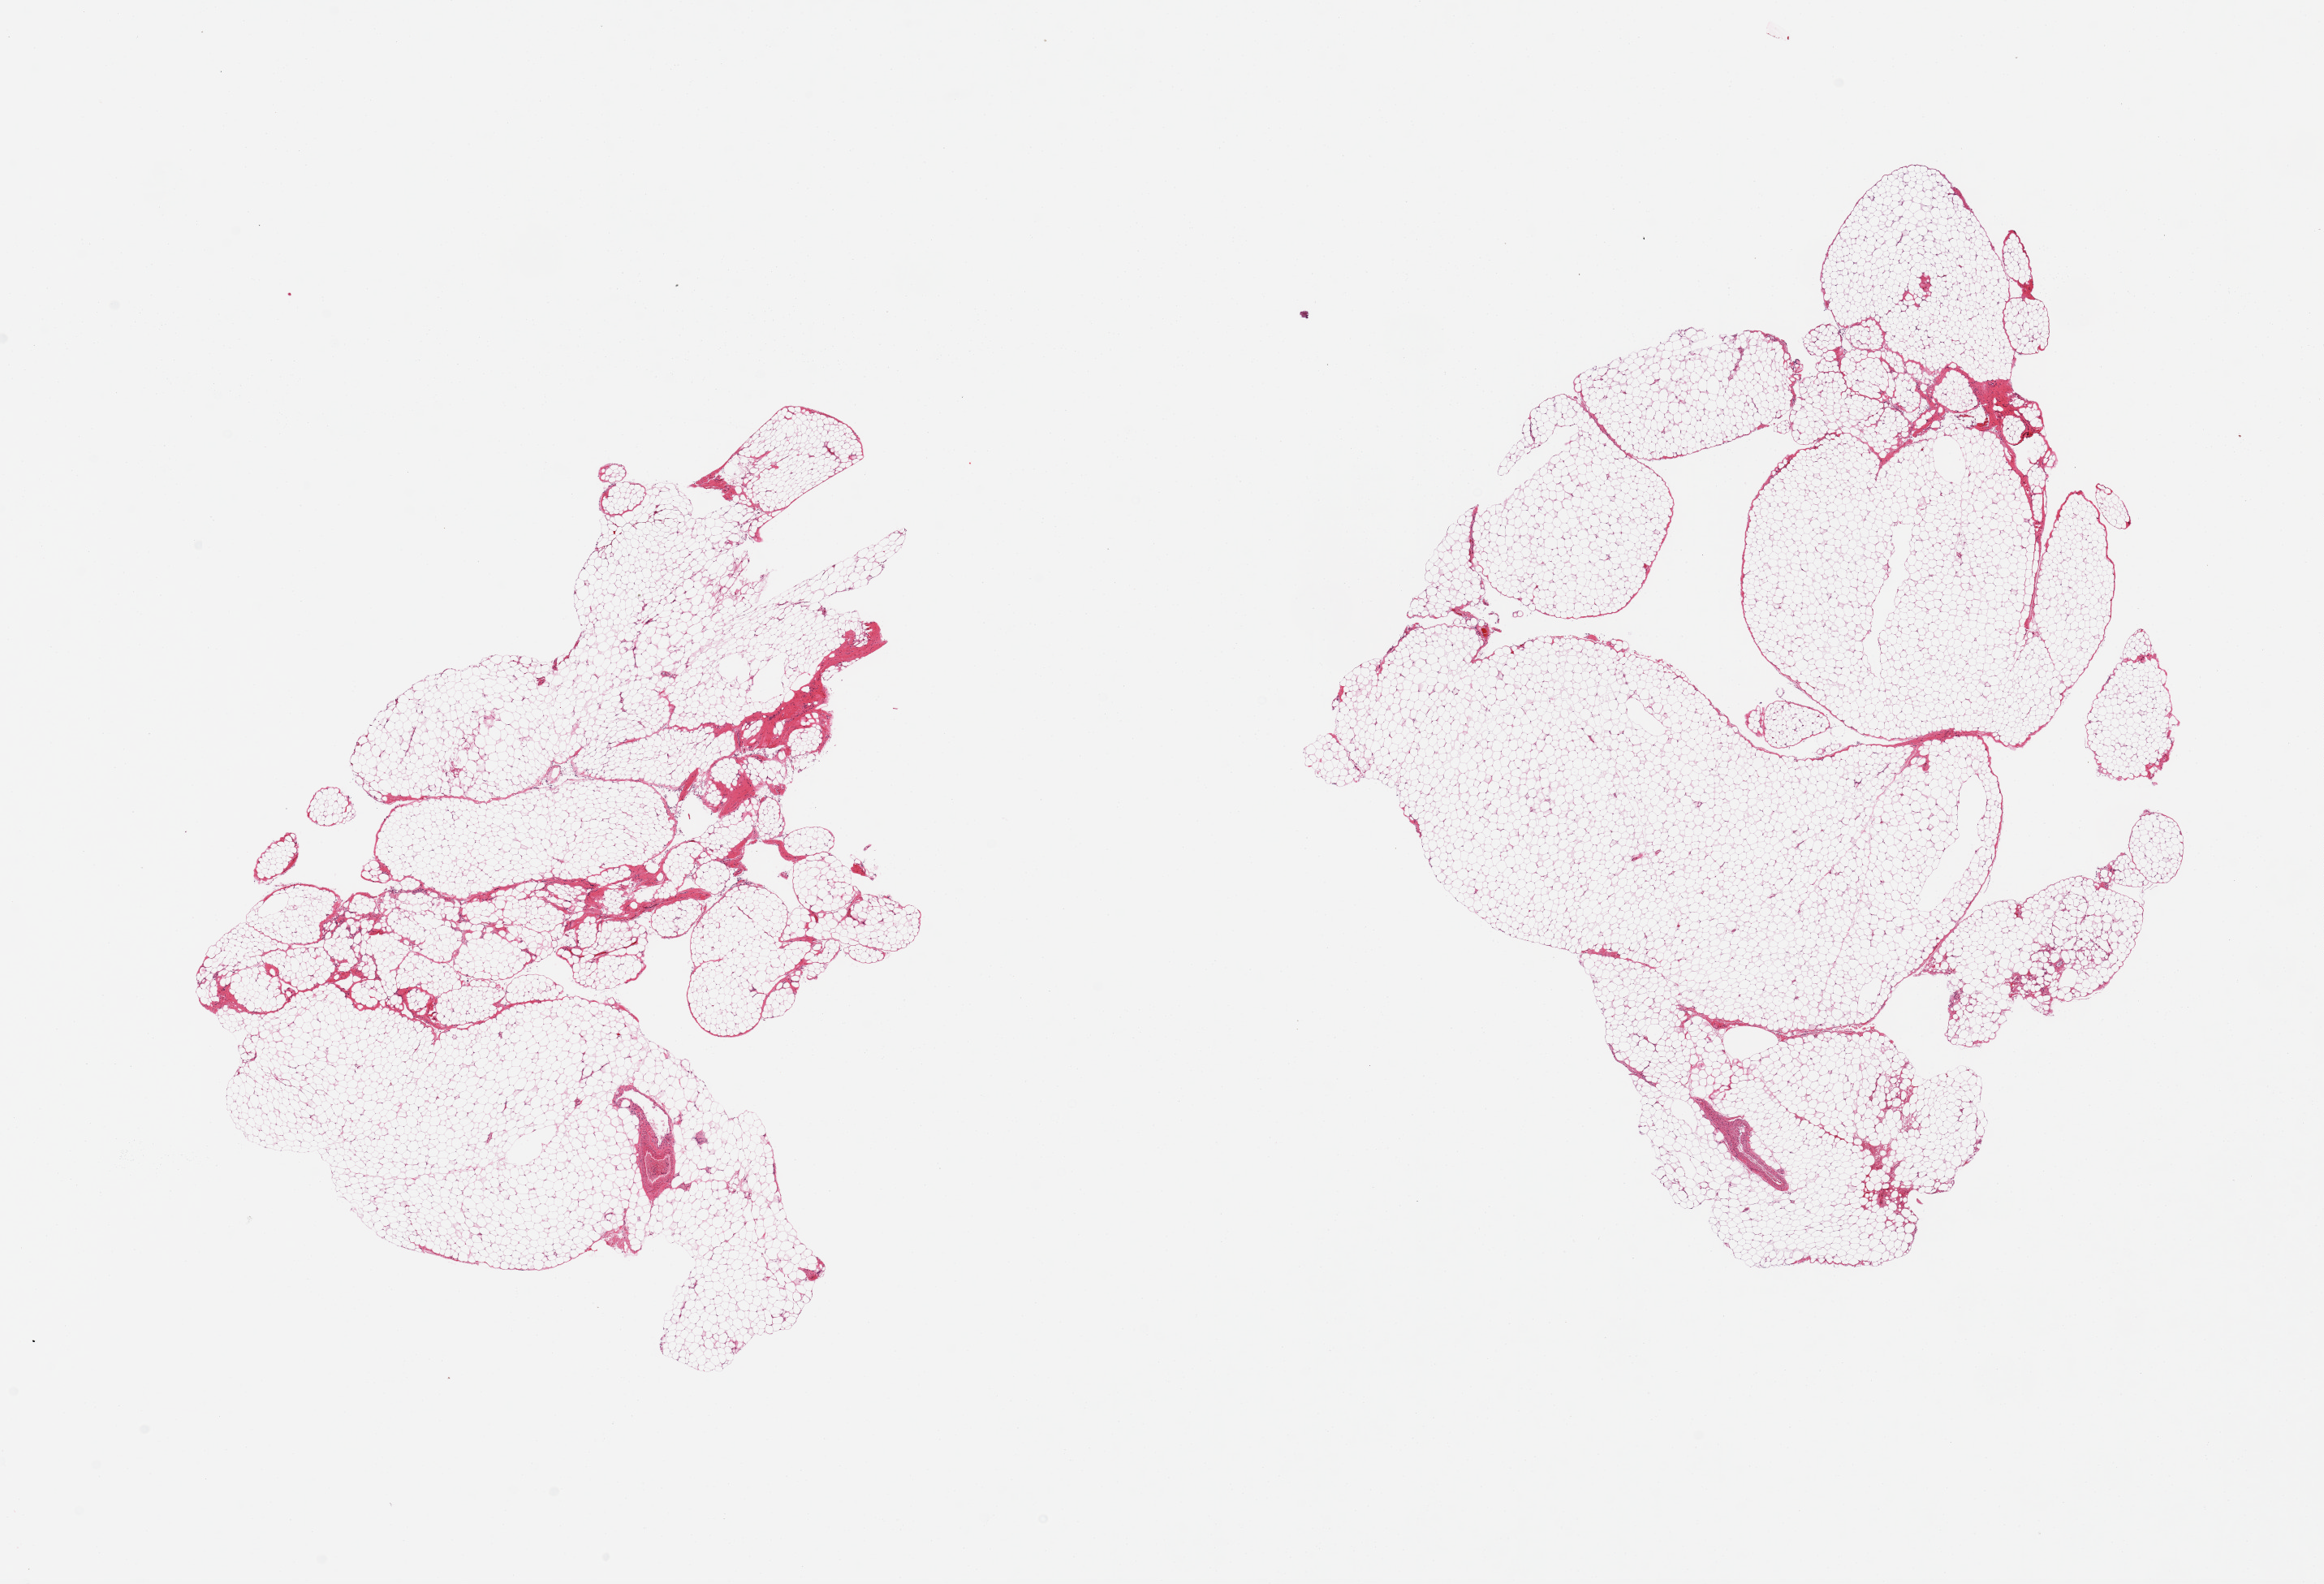
Digitized H&E-stained section — shown as a low-resolution overview of the whole scanned area (about 22.6 x 15.4 mm, acquisition: 20x scan), PAXgene-fixed paraffin-embedded (PFPE) section, sampled site (target tissue): omentum, donor tissue sample. Donor: male.
Pathologist's review note for this sample: 2 pieces, ~5-10% fascia.